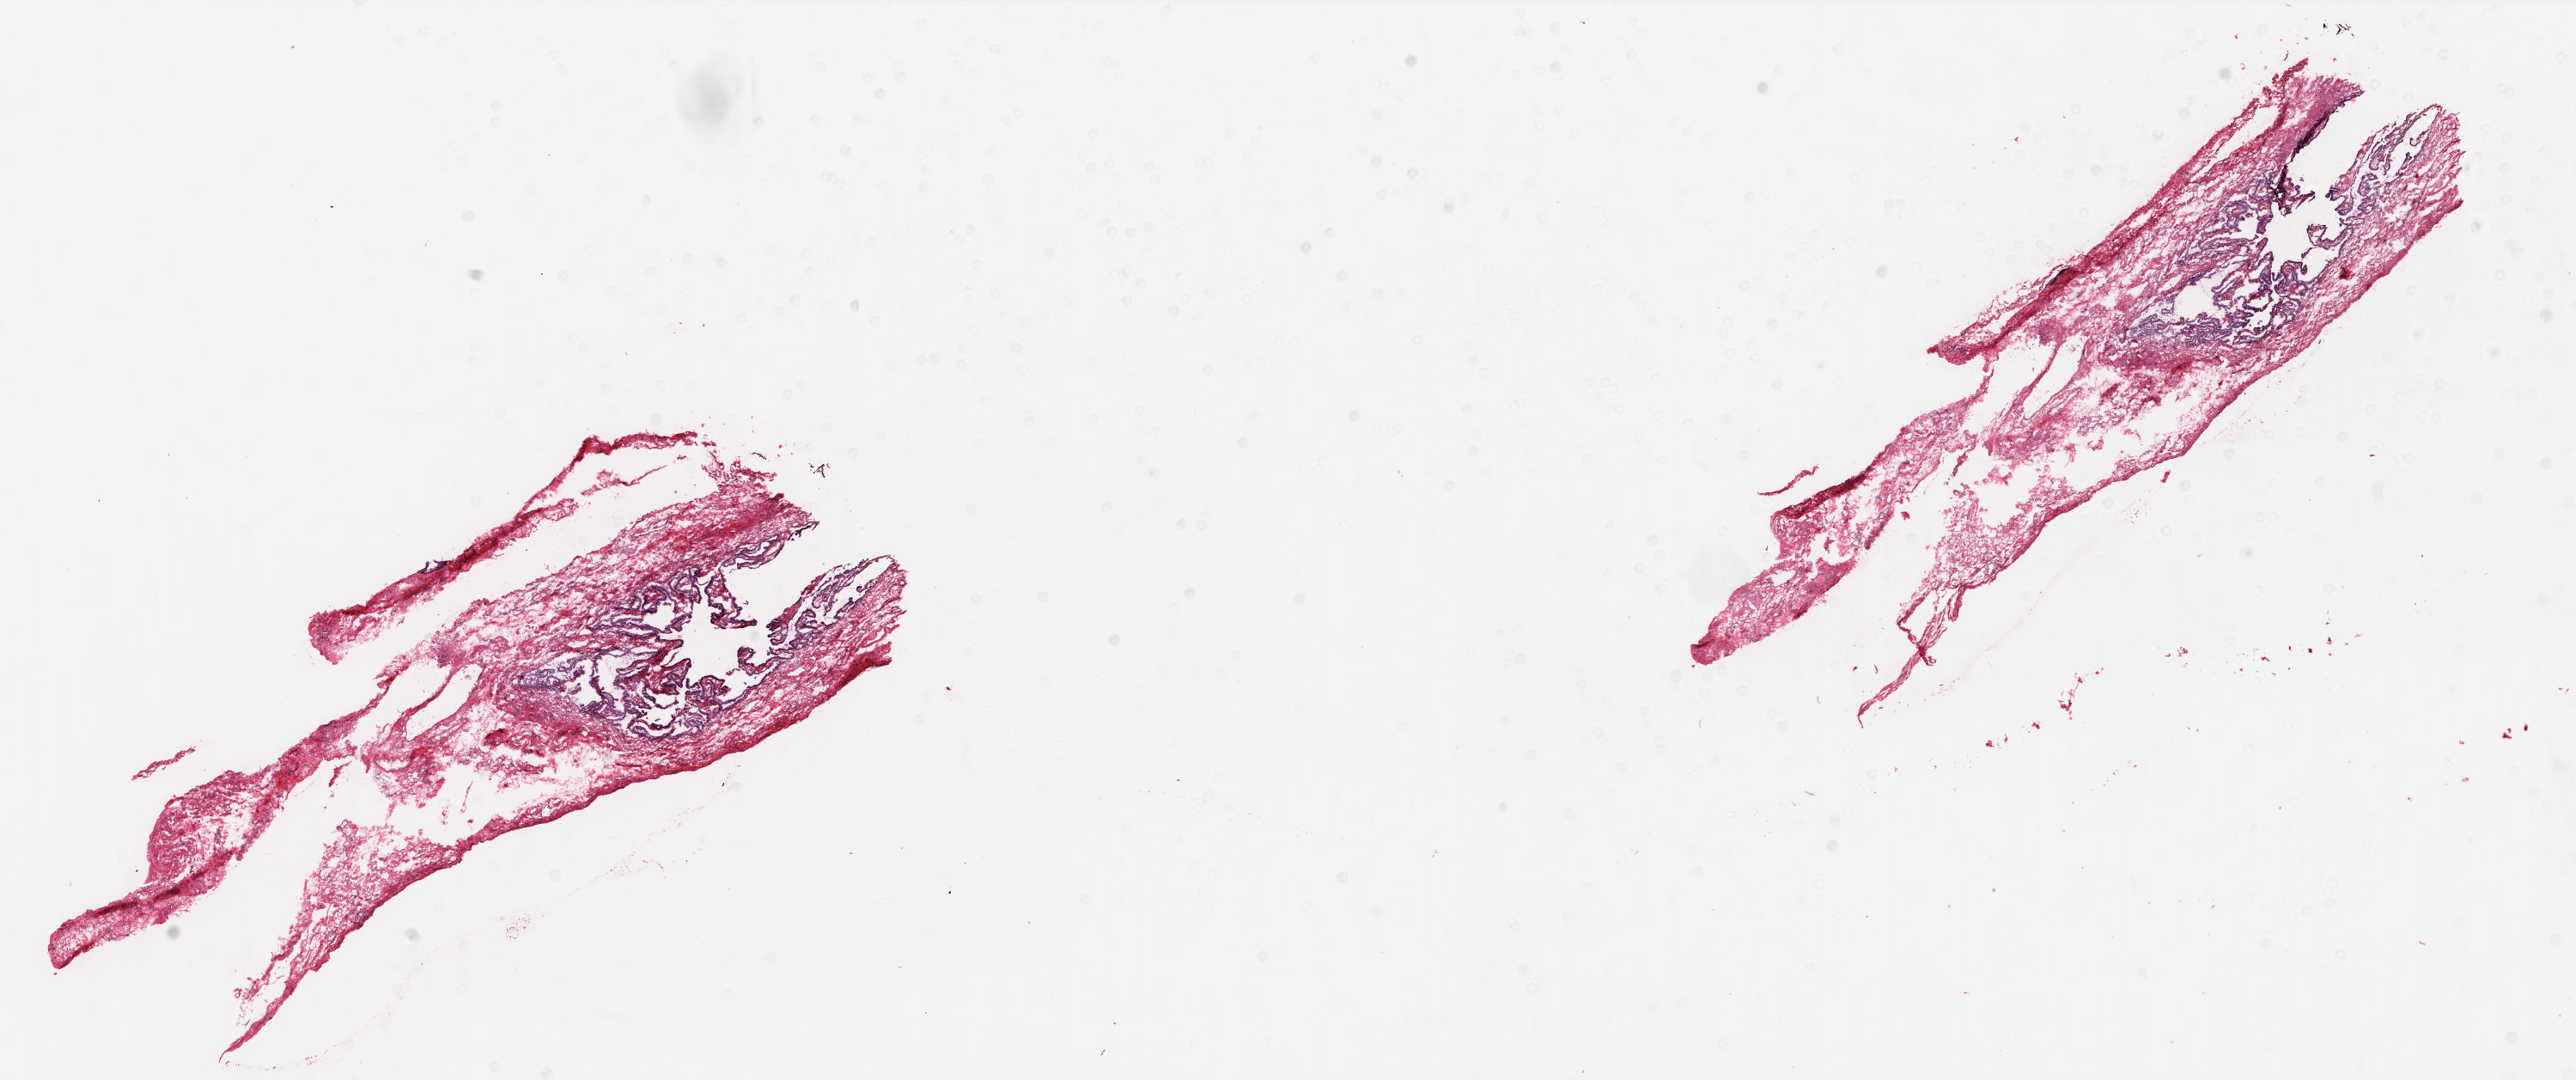
Whole-slide histology image, H&E-stained, whole scanned area (about 24.0 x 10.0 mm) shown as a low-resolution overview. Frozen section from the top of the tissue portion. Ovary, solid tissue normal (non-tumour tissue) sample. Patient: female, age at initial diagnosis 48 years.
This section: solid tissue normal (non-tumour) sample from the same patient. Patient diagnosis: Serous cystadenocarcinoma, NOS.